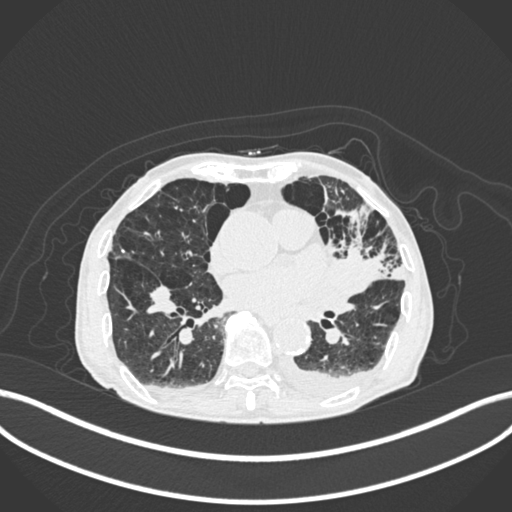
Chest CT, one axial slice. Position 92 of 400 along the scan axis. 120 kVp. Lung window (W 1500 / L -600 HU). 1 mm slice thickness. 512 × 512 image matrix, field of view 400 × 400 mm. Male patient, age 90 years or older. From the clinical record (not read from this slice): clinical TNM (as recorded): T2b N1 M0.
Structures marked on this image (rectangle marked by the reading radiologist):
- lung tumour (recorded histology: squamous cell carcinoma): bounding box <317,230,387,297> (left, top, right, bottom; pixels)